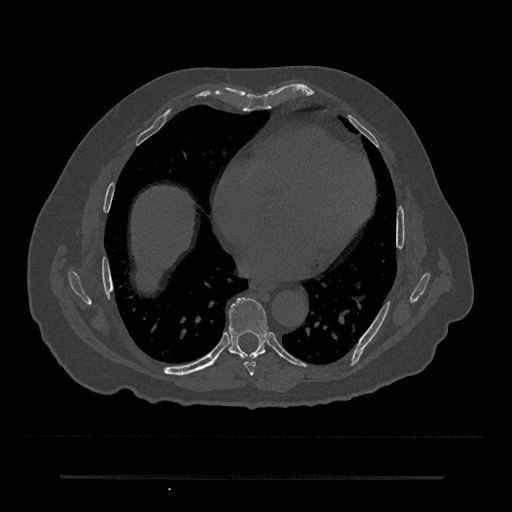
CT including the spine, one axial slice; slice 354 of 797 in the series (ordered by position); 120 kVp; bone window (W 1800 / L 400 HU); 0.5 mm slice thickness; 512 × 512 image matrix, field of view 437 × 437 mm. Patient: male, 69 years. From the clinical record (not read from this slice): primary cancer: prostate.
Annotated regions visible in this slice (semi-automatic segmentation, software-assisted and operator-edited):
- T7 vertebra: bounding box <244,361,256,376> (left, top, right, bottom; pixels)
- T8 vertebra: <229,297,267,359>